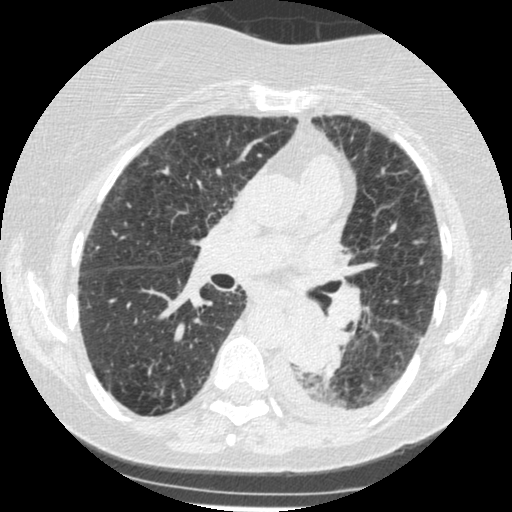
Chest CT (low-dose screening protocol), one axial image, third annual screen, lung window (W 1500 / L -600 HU), 1.25 mm slice thickness, slice 202 of 341 in the series. Female, age 60 years at enrolment.
• Expert reader's lesion annotation, bounding box [x1, y1, x2, y2] px = [271, 307, 342, 374].
• Screening reader's record for this exam (one nodule recorded; not confirmed to be the boxed lesion): non-calcified nodule or mass ≥4 mm, left lower lobe, 54 × 38 mm, smooth margins, soft tissue attenuation, pre-existing on the prior screen: yes; interval growth: yes.
• Later outcome: lung cancer diagnosed 15 days after this screen — small cell carcinoma, NOS, left lower lobe, undifferentiated (G4), stage IV (AJCC 6th edition), 69 mm at pathology.